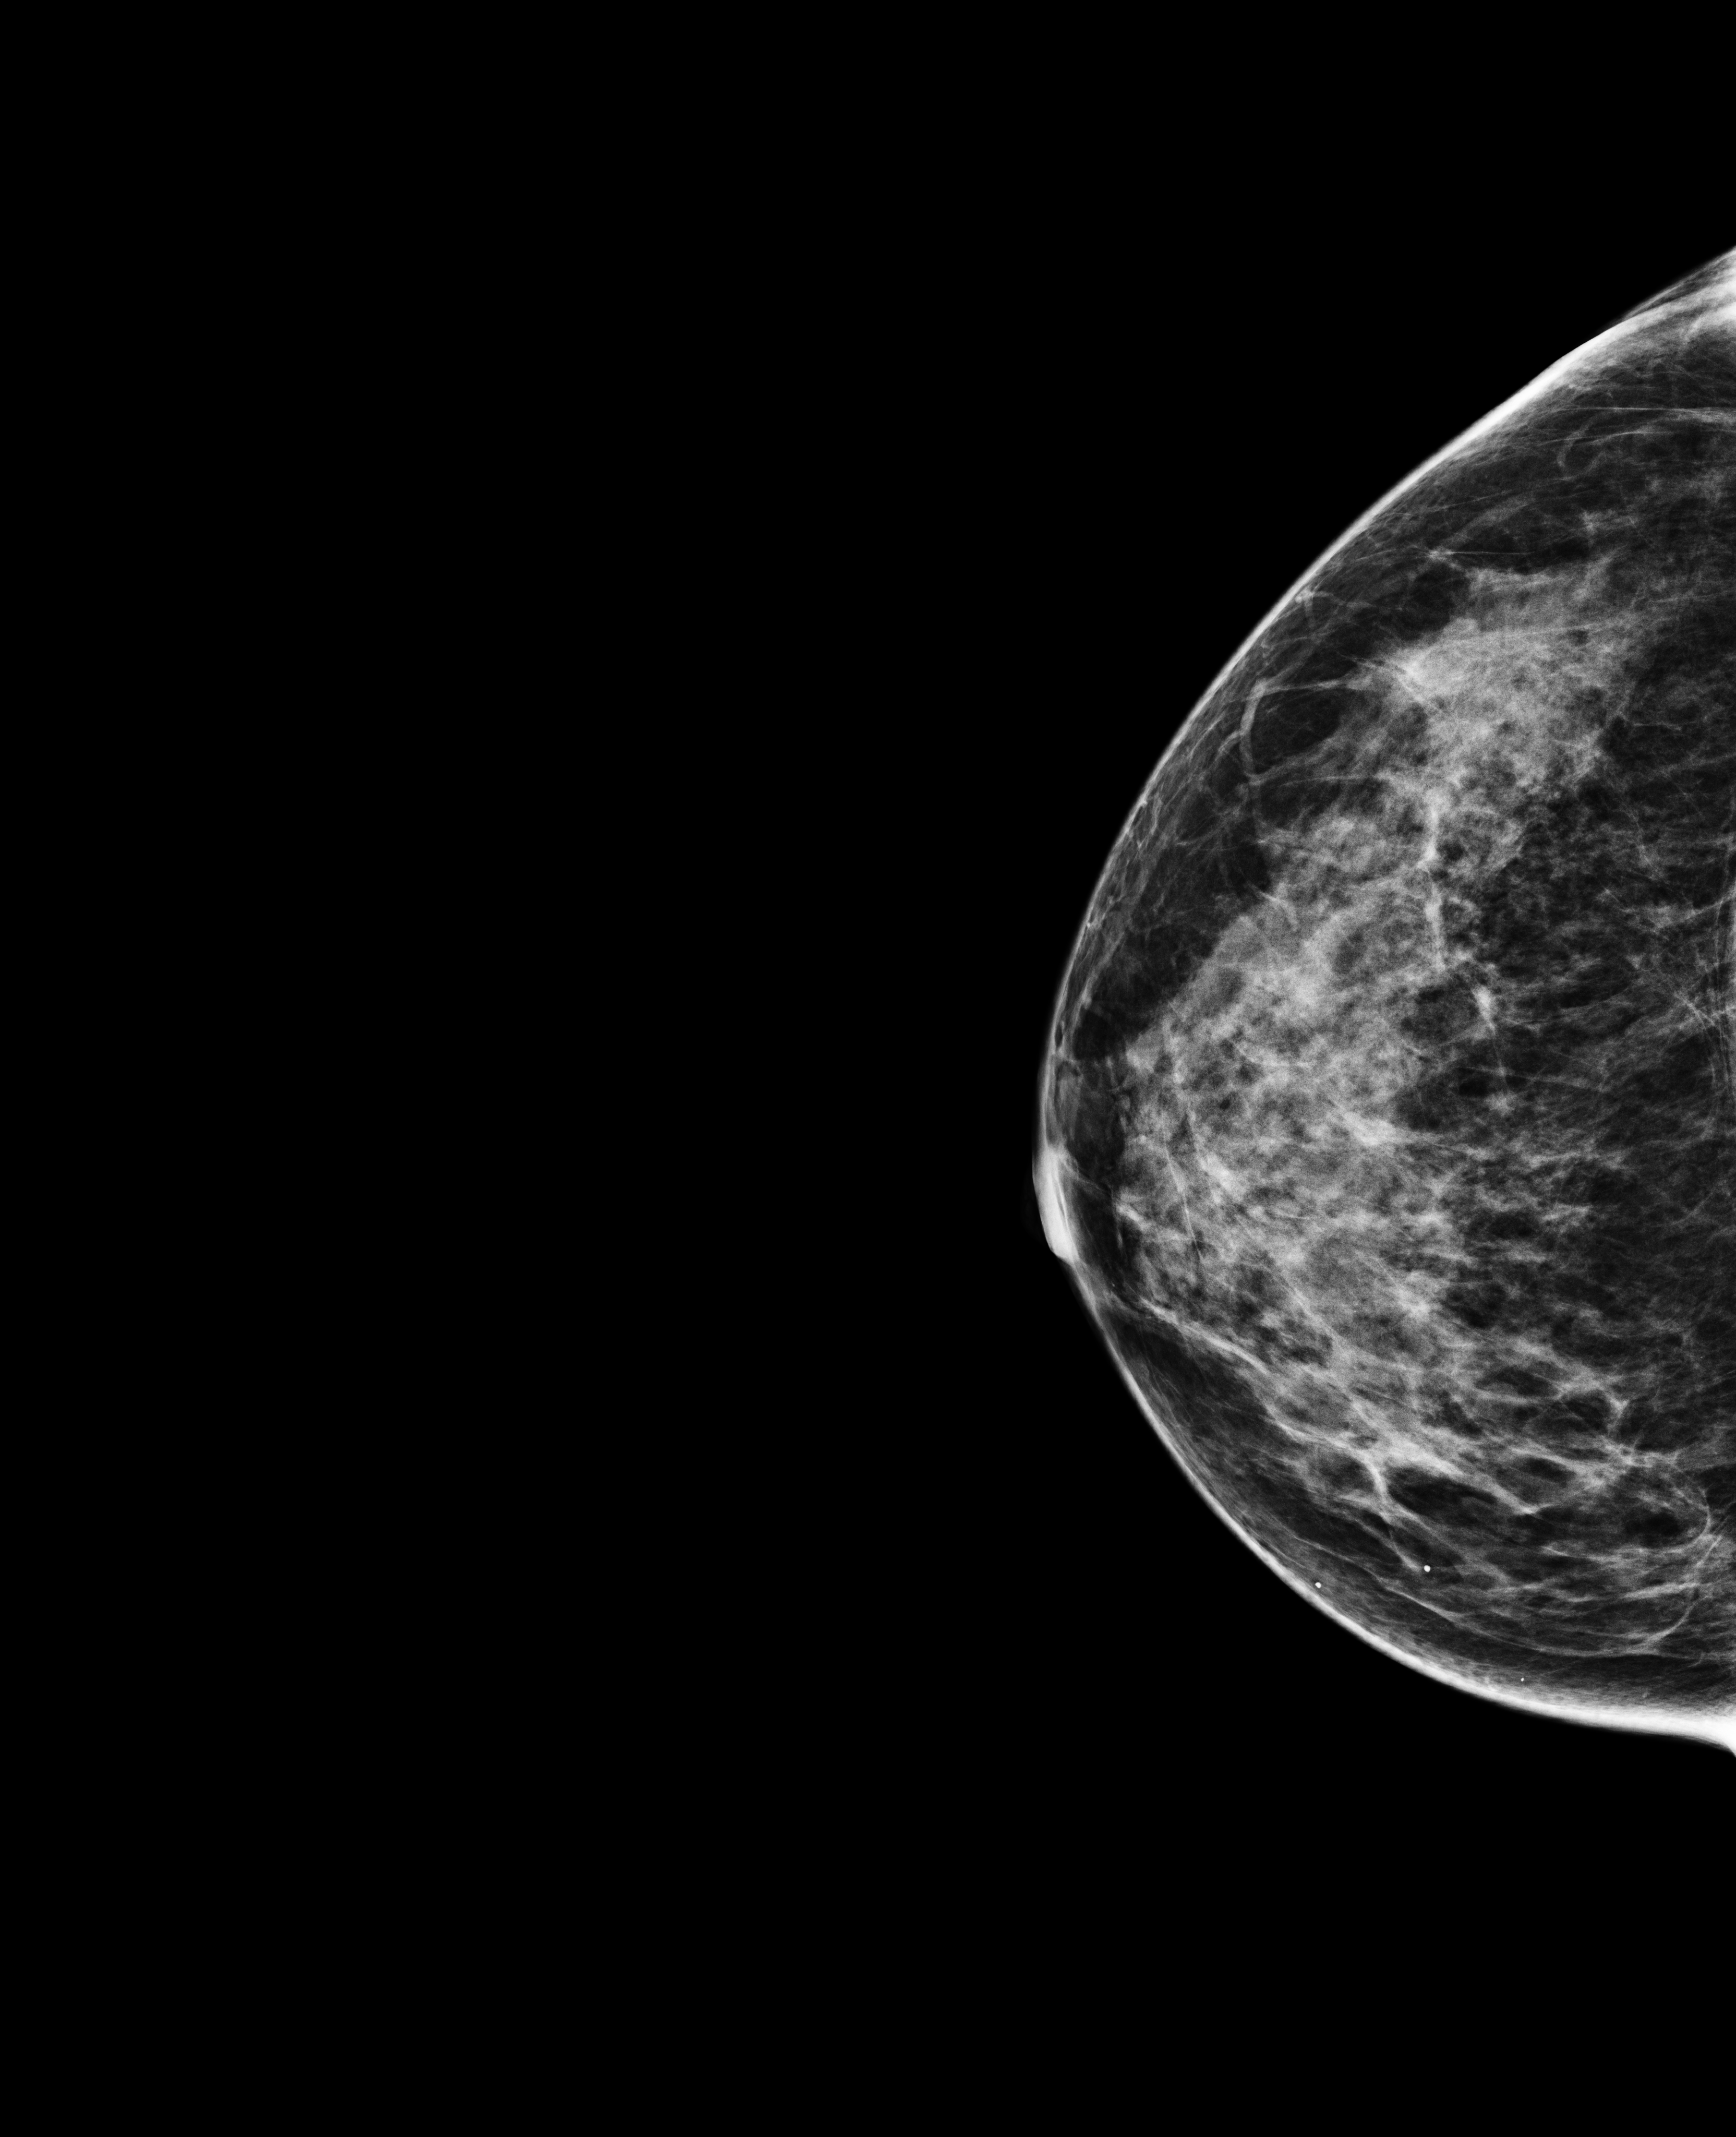
Full-field digital mammogram (FFDM), right breast, cranio-caudal projection, annual screening mammography examination, compressed breast thickness 52 mm. Female patient, age 46 years.
Breast density at the screening exam (both breasts): heterogeneously dense (BI-RADS density category c). Final BI-RADS category for the screening round (tomosynthesis exam, both breasts): category 1. Recall: no recall after this screen.